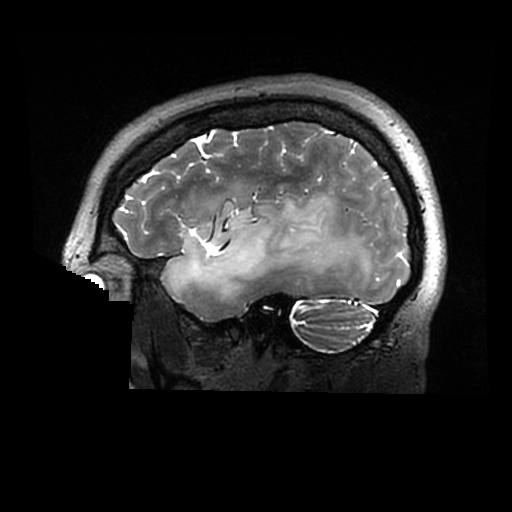
Brain MRI from a brain-tumour surgery series, one sagittal slice; slice 225 of 320 in the series (ordered by position); 512 × 512 image matrix. From the clinical record (not read from this slice): histopathology: Astrocytoma; WHO grade: 2; IDH mutation: yes.
Structures marked on this image (outlined manually by an expert reader):
- tumour: bounding box <166,194,378,300> (left, top, right, bottom; pixels)